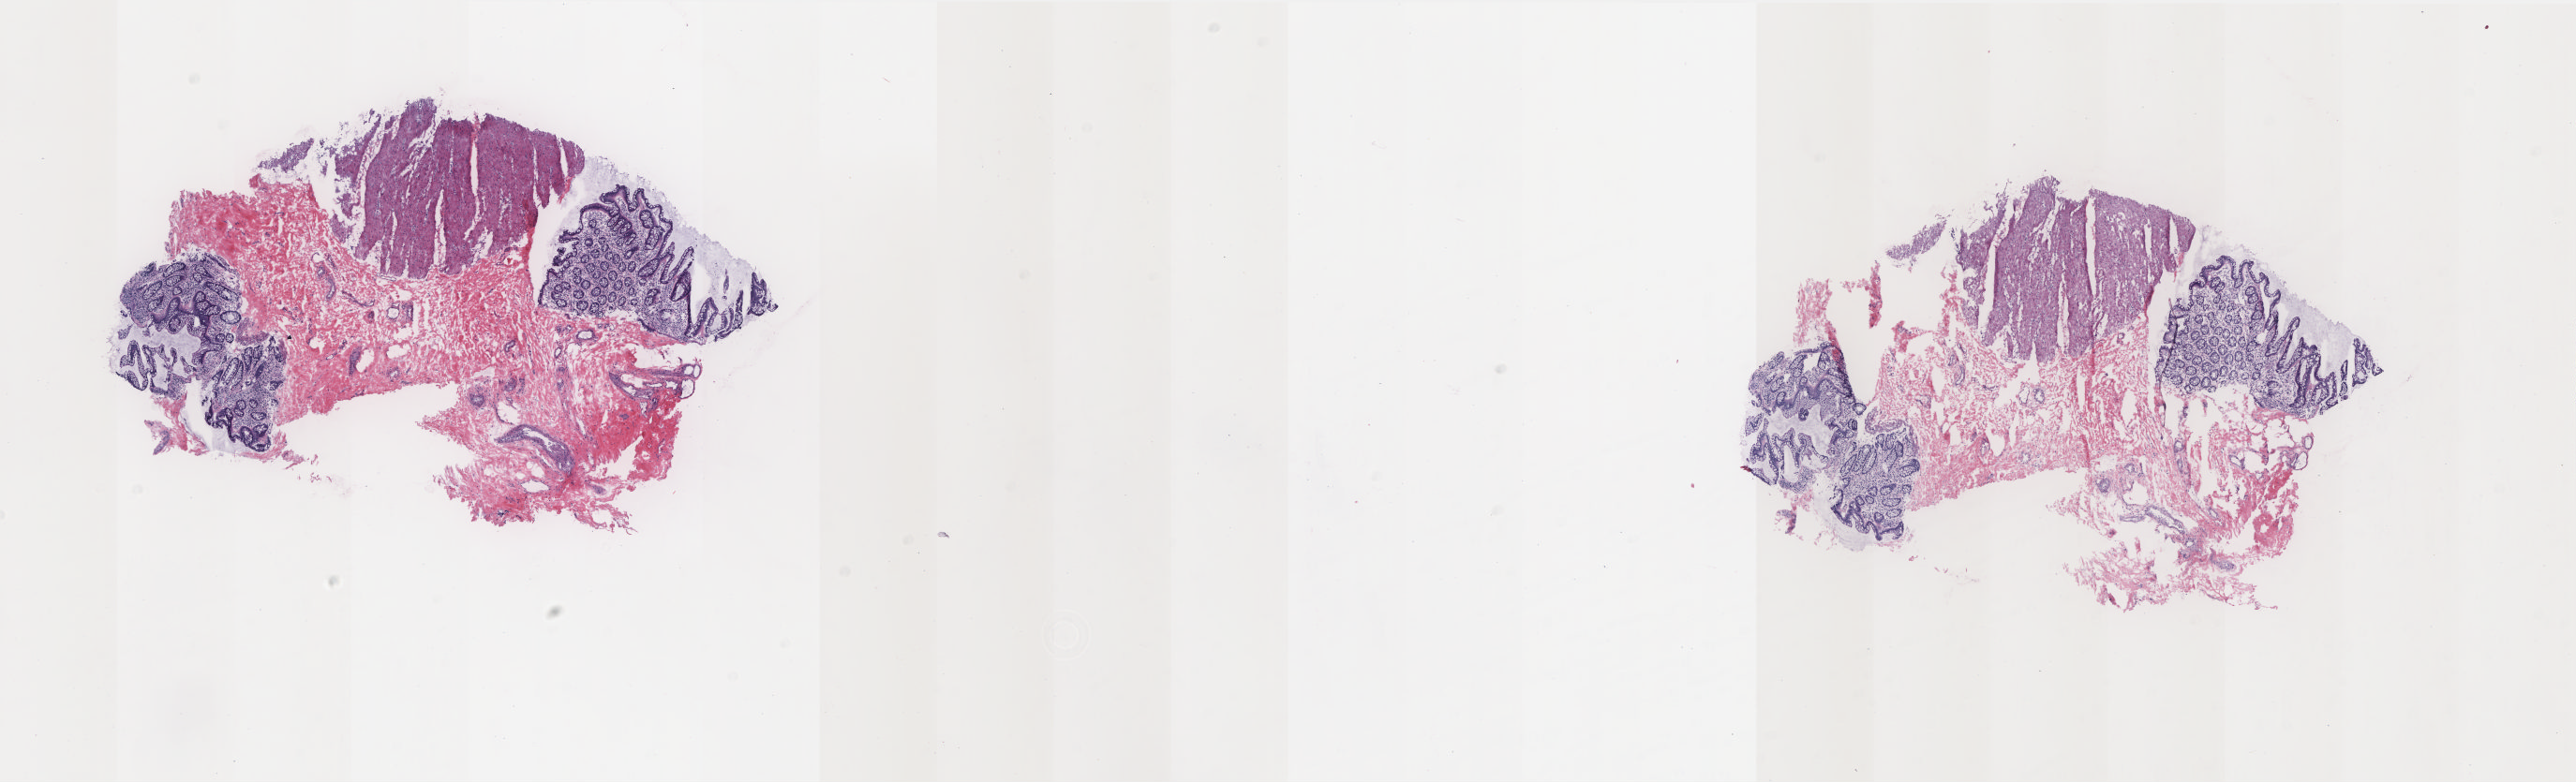
H&E whole-slide image — a low-resolution overview of the entire scanned area, about 22.0 x 6.7 mm (acquisition: 20x scan); frozen section; sample: solid tissue normal (non-tumour tissue), colon. Female, age 63 years at initial diagnosis. Composition of this section per pathologist review: tumour cells 0%, normal cells 100%. Infiltration values recorded for this section: lymphocyte infiltration 25%, monocyte infiltration 5%, neutrophil infiltration 0%.
• this section: solid tissue normal sample (biorepository sample class)
• patient diagnosis: Adenocarcinoma, NOS (sigmoid colon)